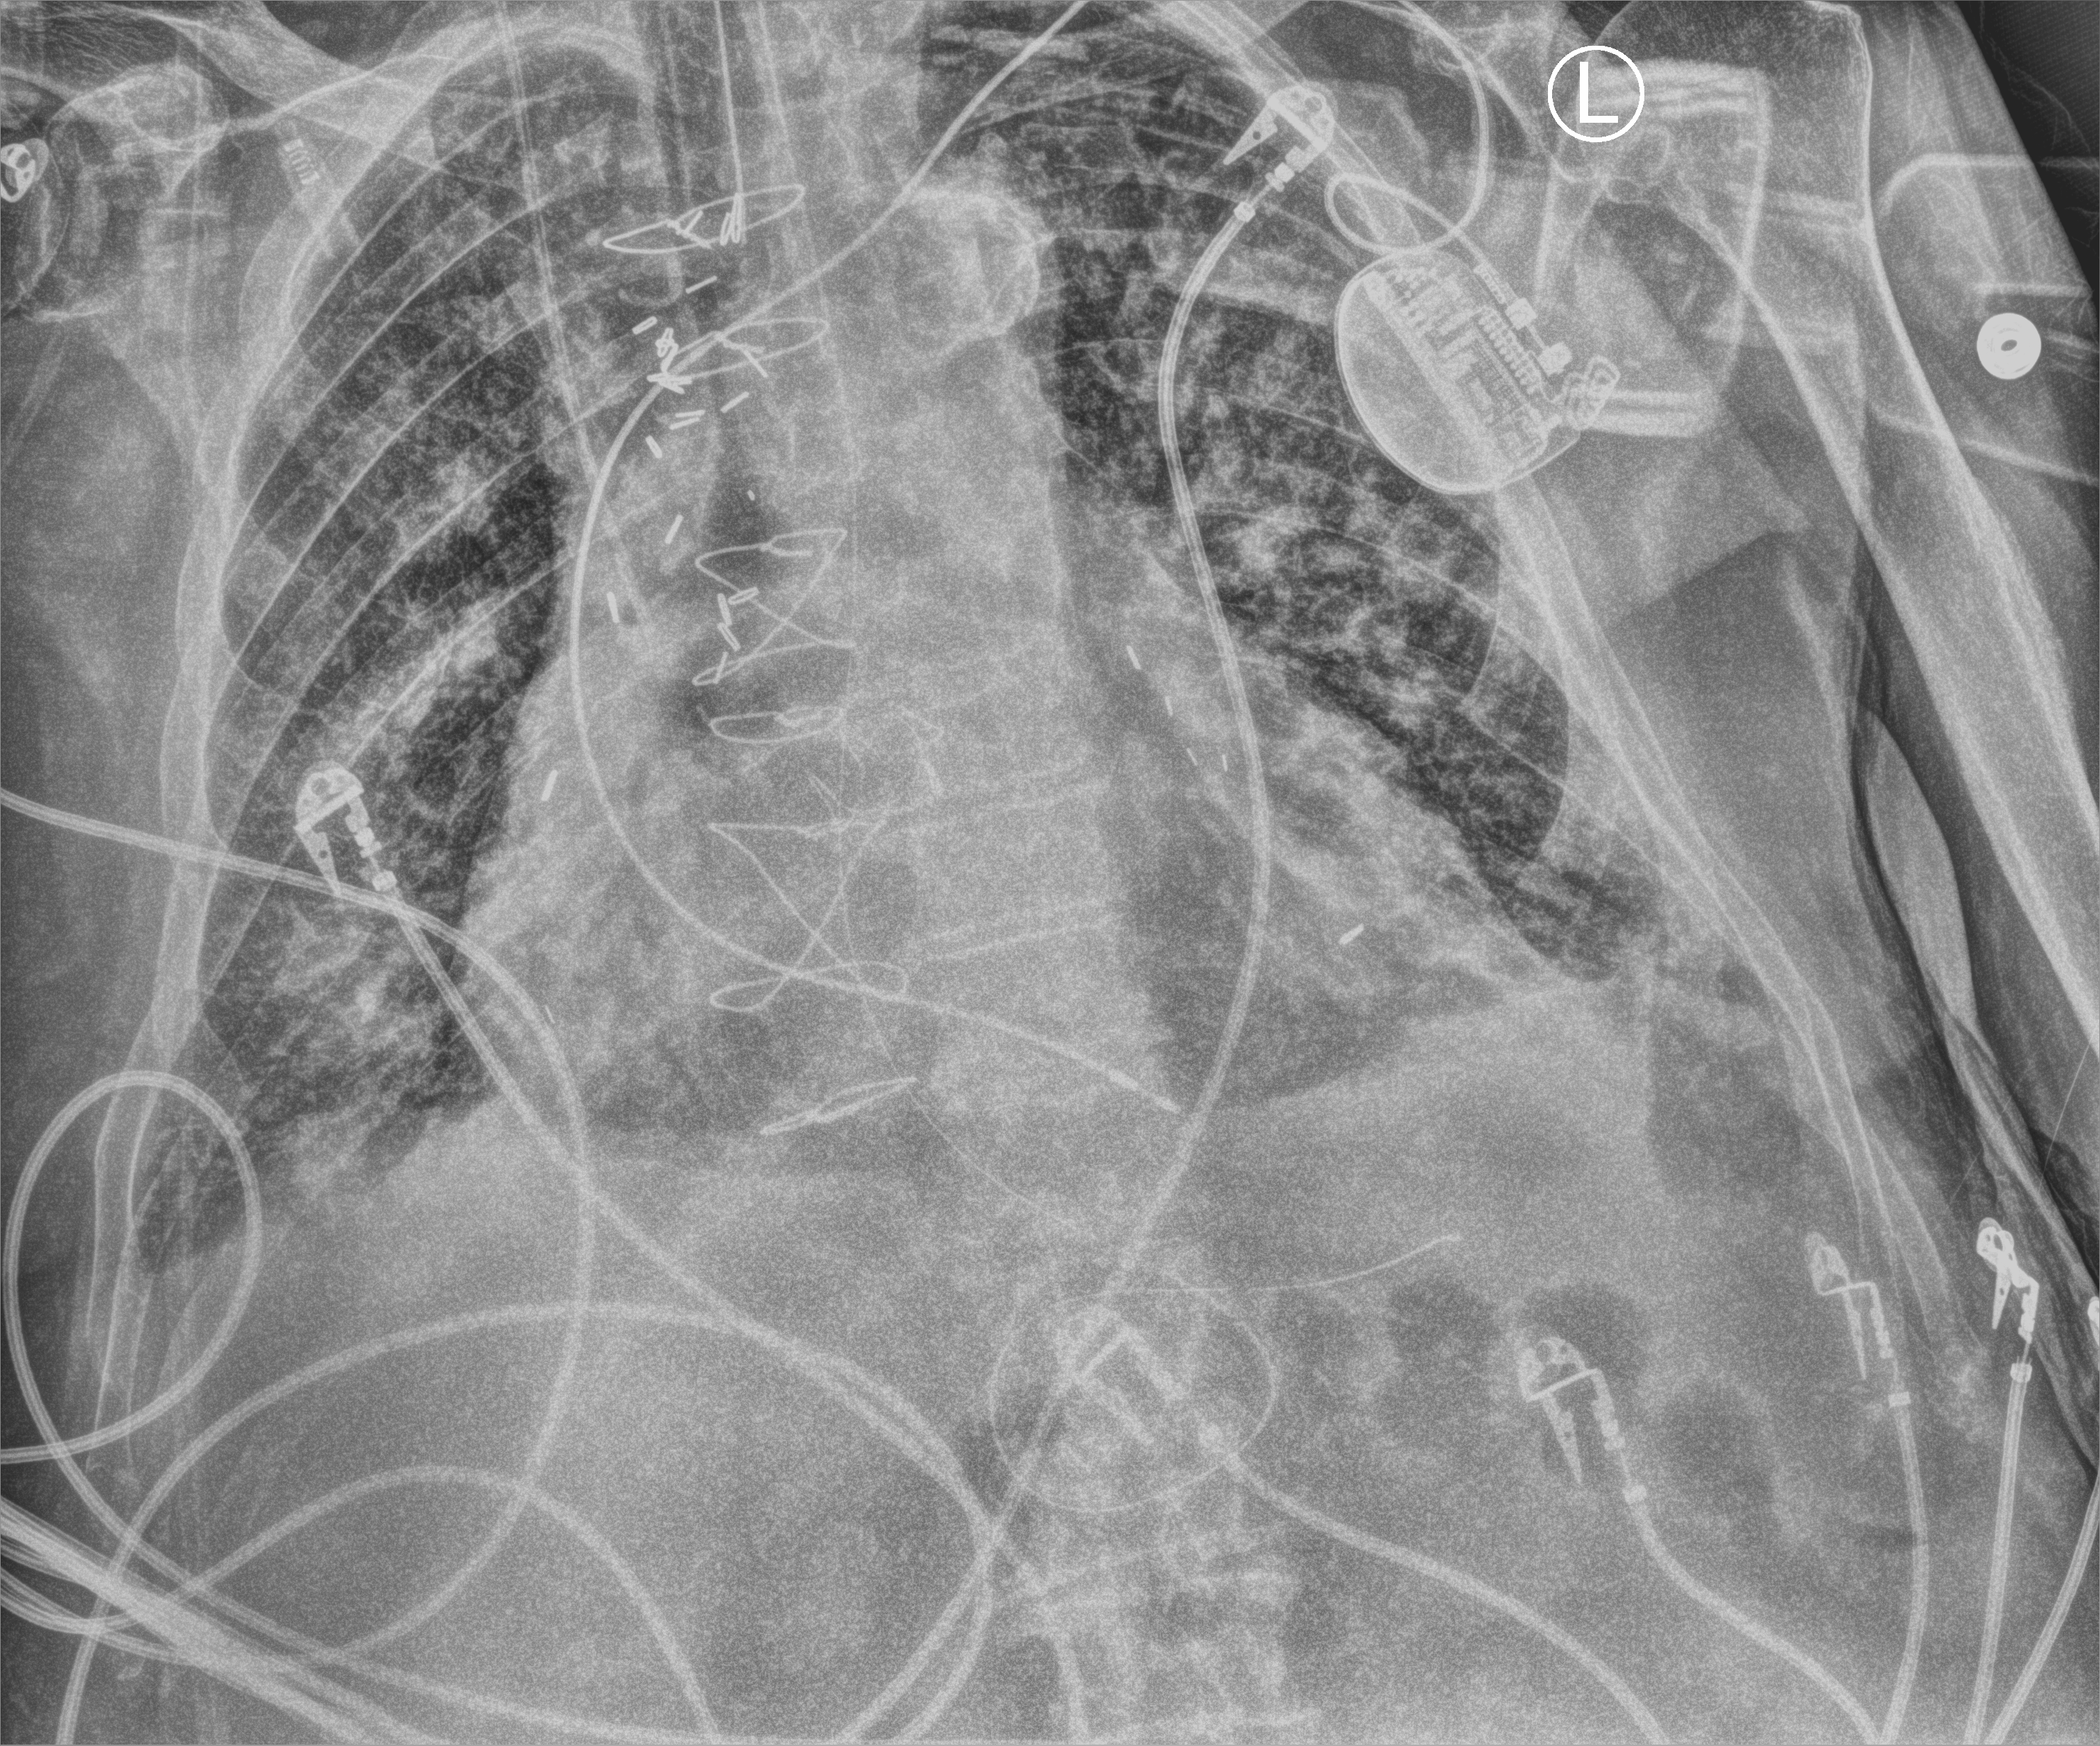
Portable chest radiograph; anteroposterior (AP) projection. Male patient hospitalised with COVID-19, age 75–90 years.
Hospital-stay facts (about this admission, not read from this image; timing relative to this image not recorded): chronic kidney disease (admission record): no; other chronic lung disease (admission record): yes.